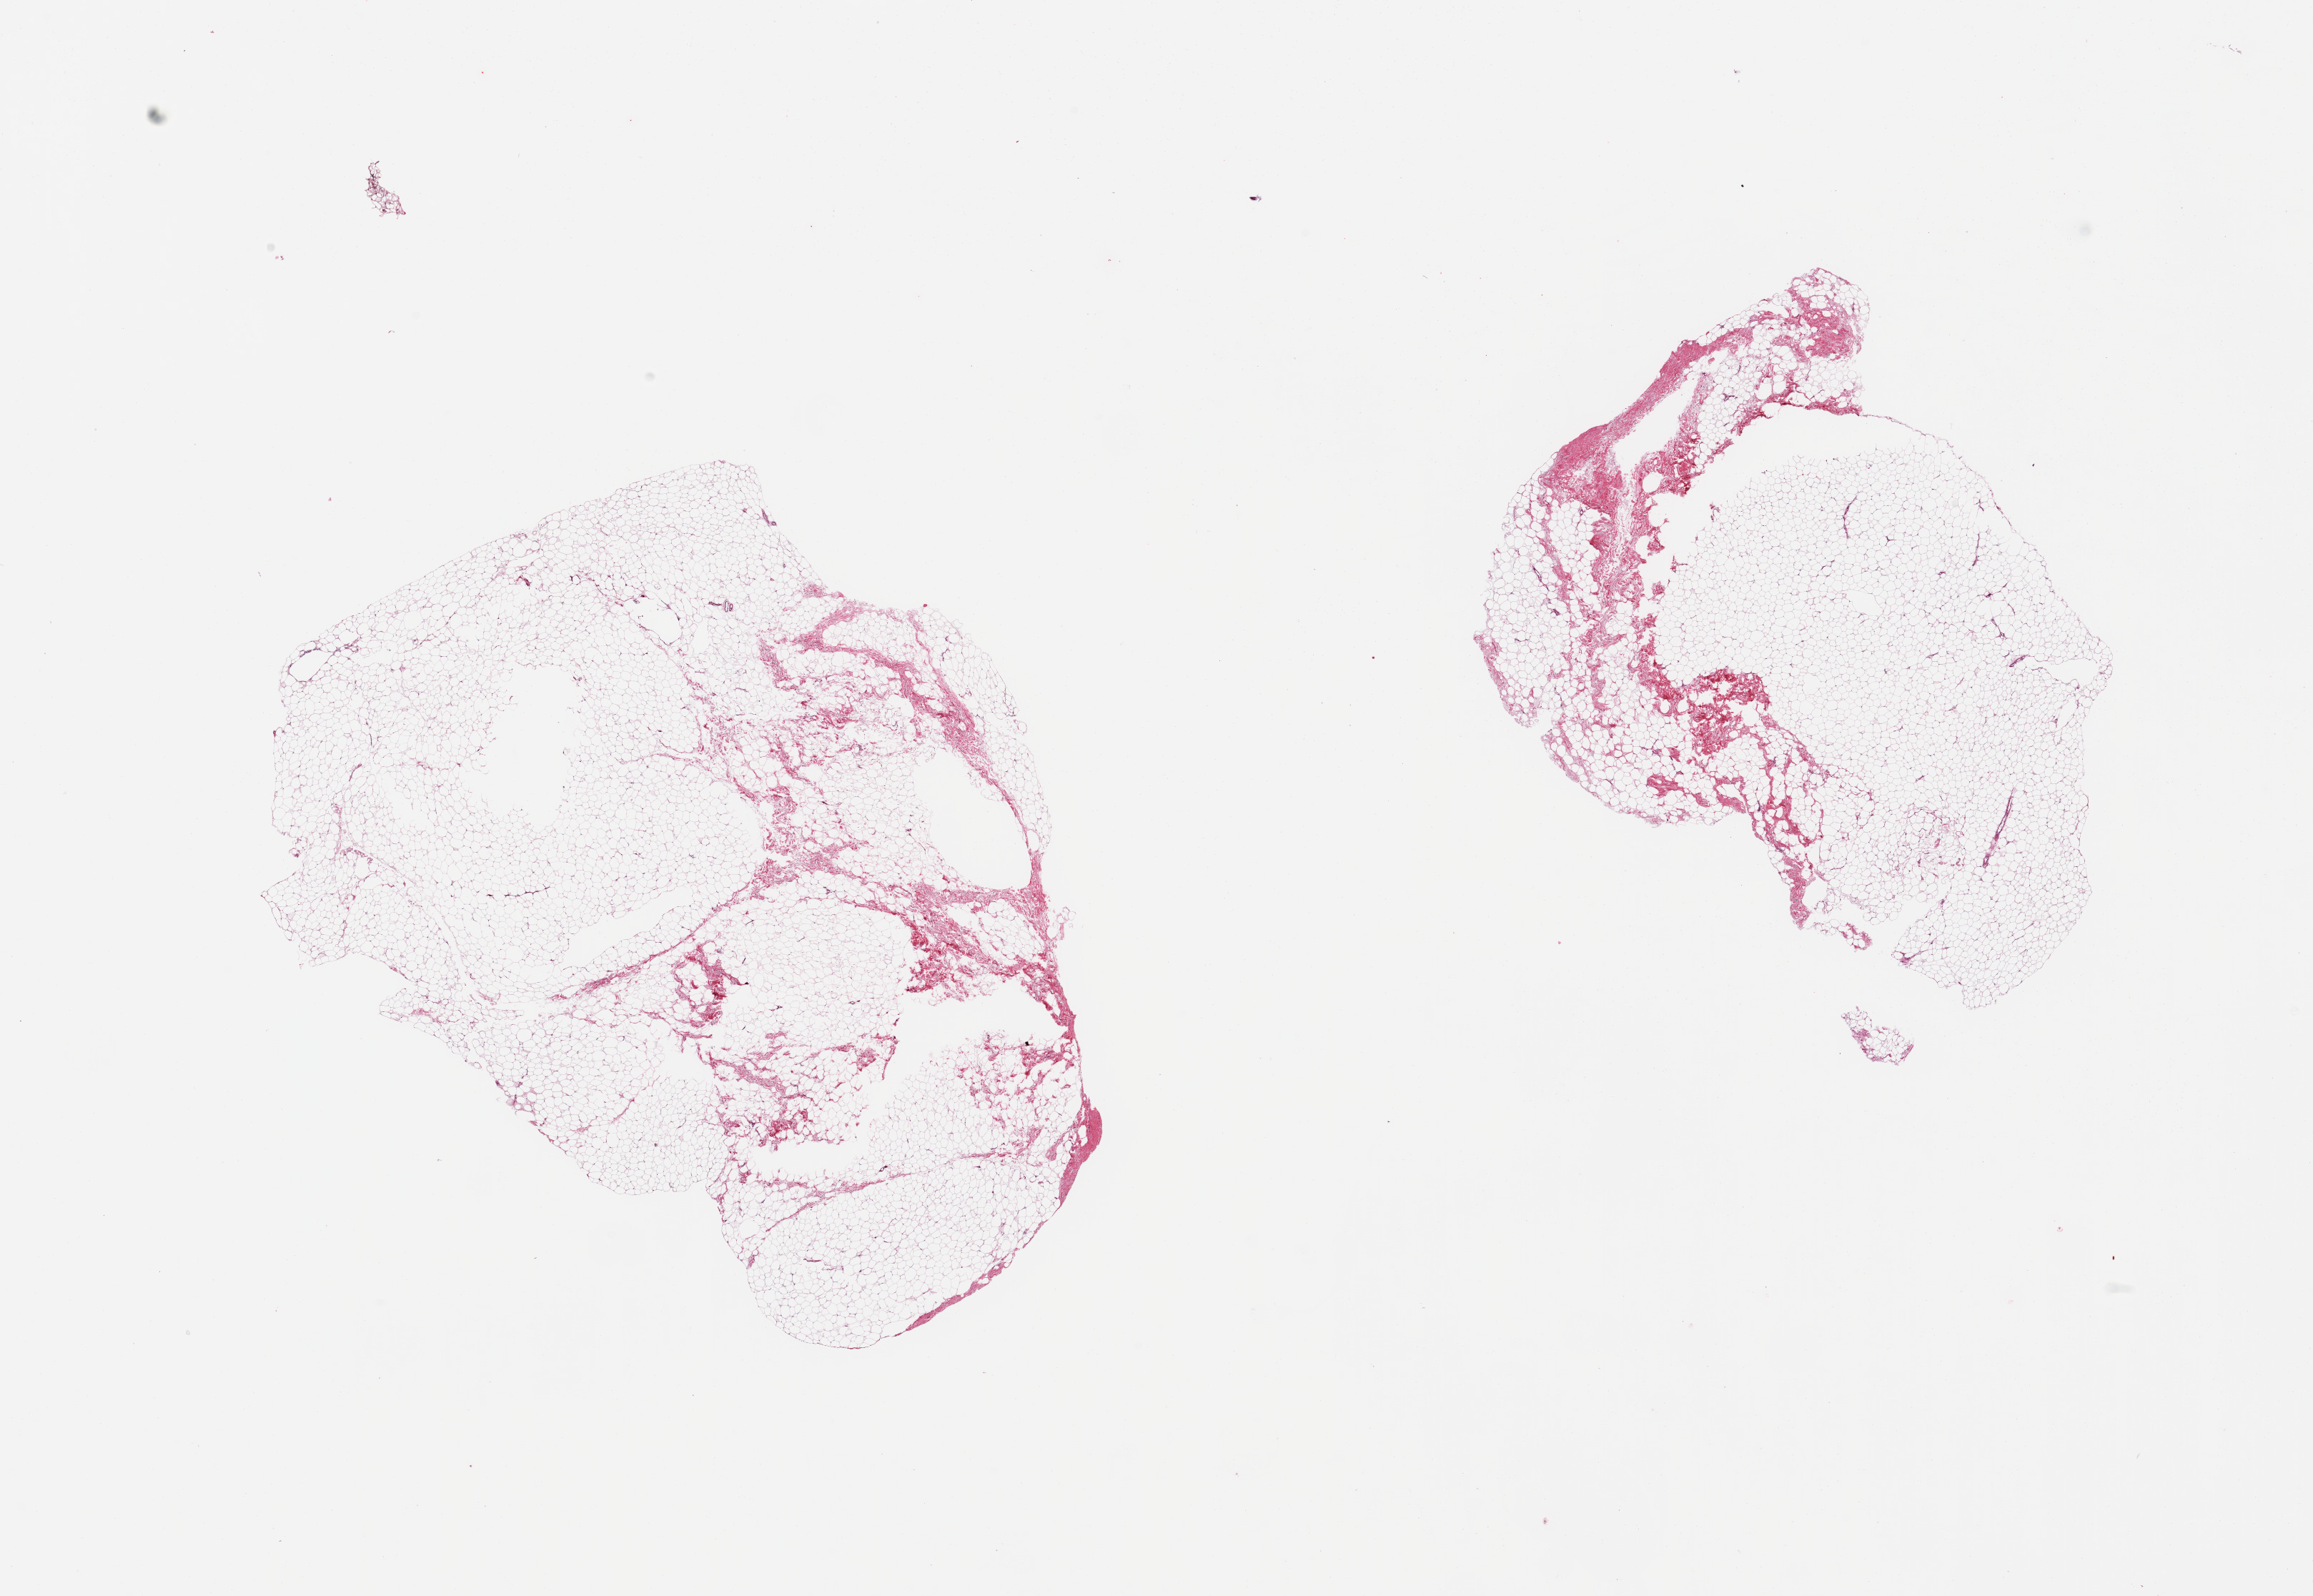
Whole-slide image, H&E stain, brightfield — low-resolution overview of the scanned area, about 25.6 x 17.7 mm (acquisition: 20x scan). PAXgene-fixed paraffin-embedded (PFPE) section. Section of breast (target tissue). Tissue donor sample. Male donor.
Reviewer comment on this tissue sample: 2 pieces; fibrofatty tissue without mammary ducts.